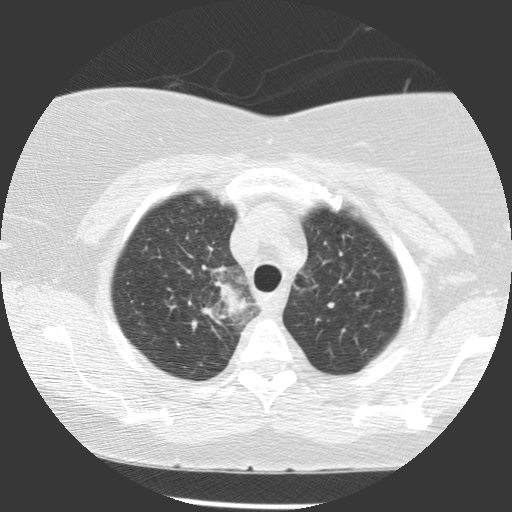
Chest CT (low-dose screening protocol), one axial image, baseline screening round, lung window (W 1500 / L -600 HU), standard (soft-tissue) reconstruction kernel (STANDARD), 140 kVp, slice 93 of 116 in the series. Female participant, aged 63 years at enrolment. Former smoker at enrolment.
Expert reader's lesion annotation, bounding box (x1, y1, x2, y2) in pixels: (202, 267, 260, 330). Reader record for this screening exam (exam-level; its link to the box is not recorded): non-calcified nodule or mass ≥4 mm, right upper lobe, 39 × 36 mm, spiculated (stellate) margins, soft tissue attenuation. Official screen result: positive, change unspecified: nodule(s) >= 4 mm or enlarging nodule(s), mass(es), or other non-specific abnormalities suspicious for lung cancer.